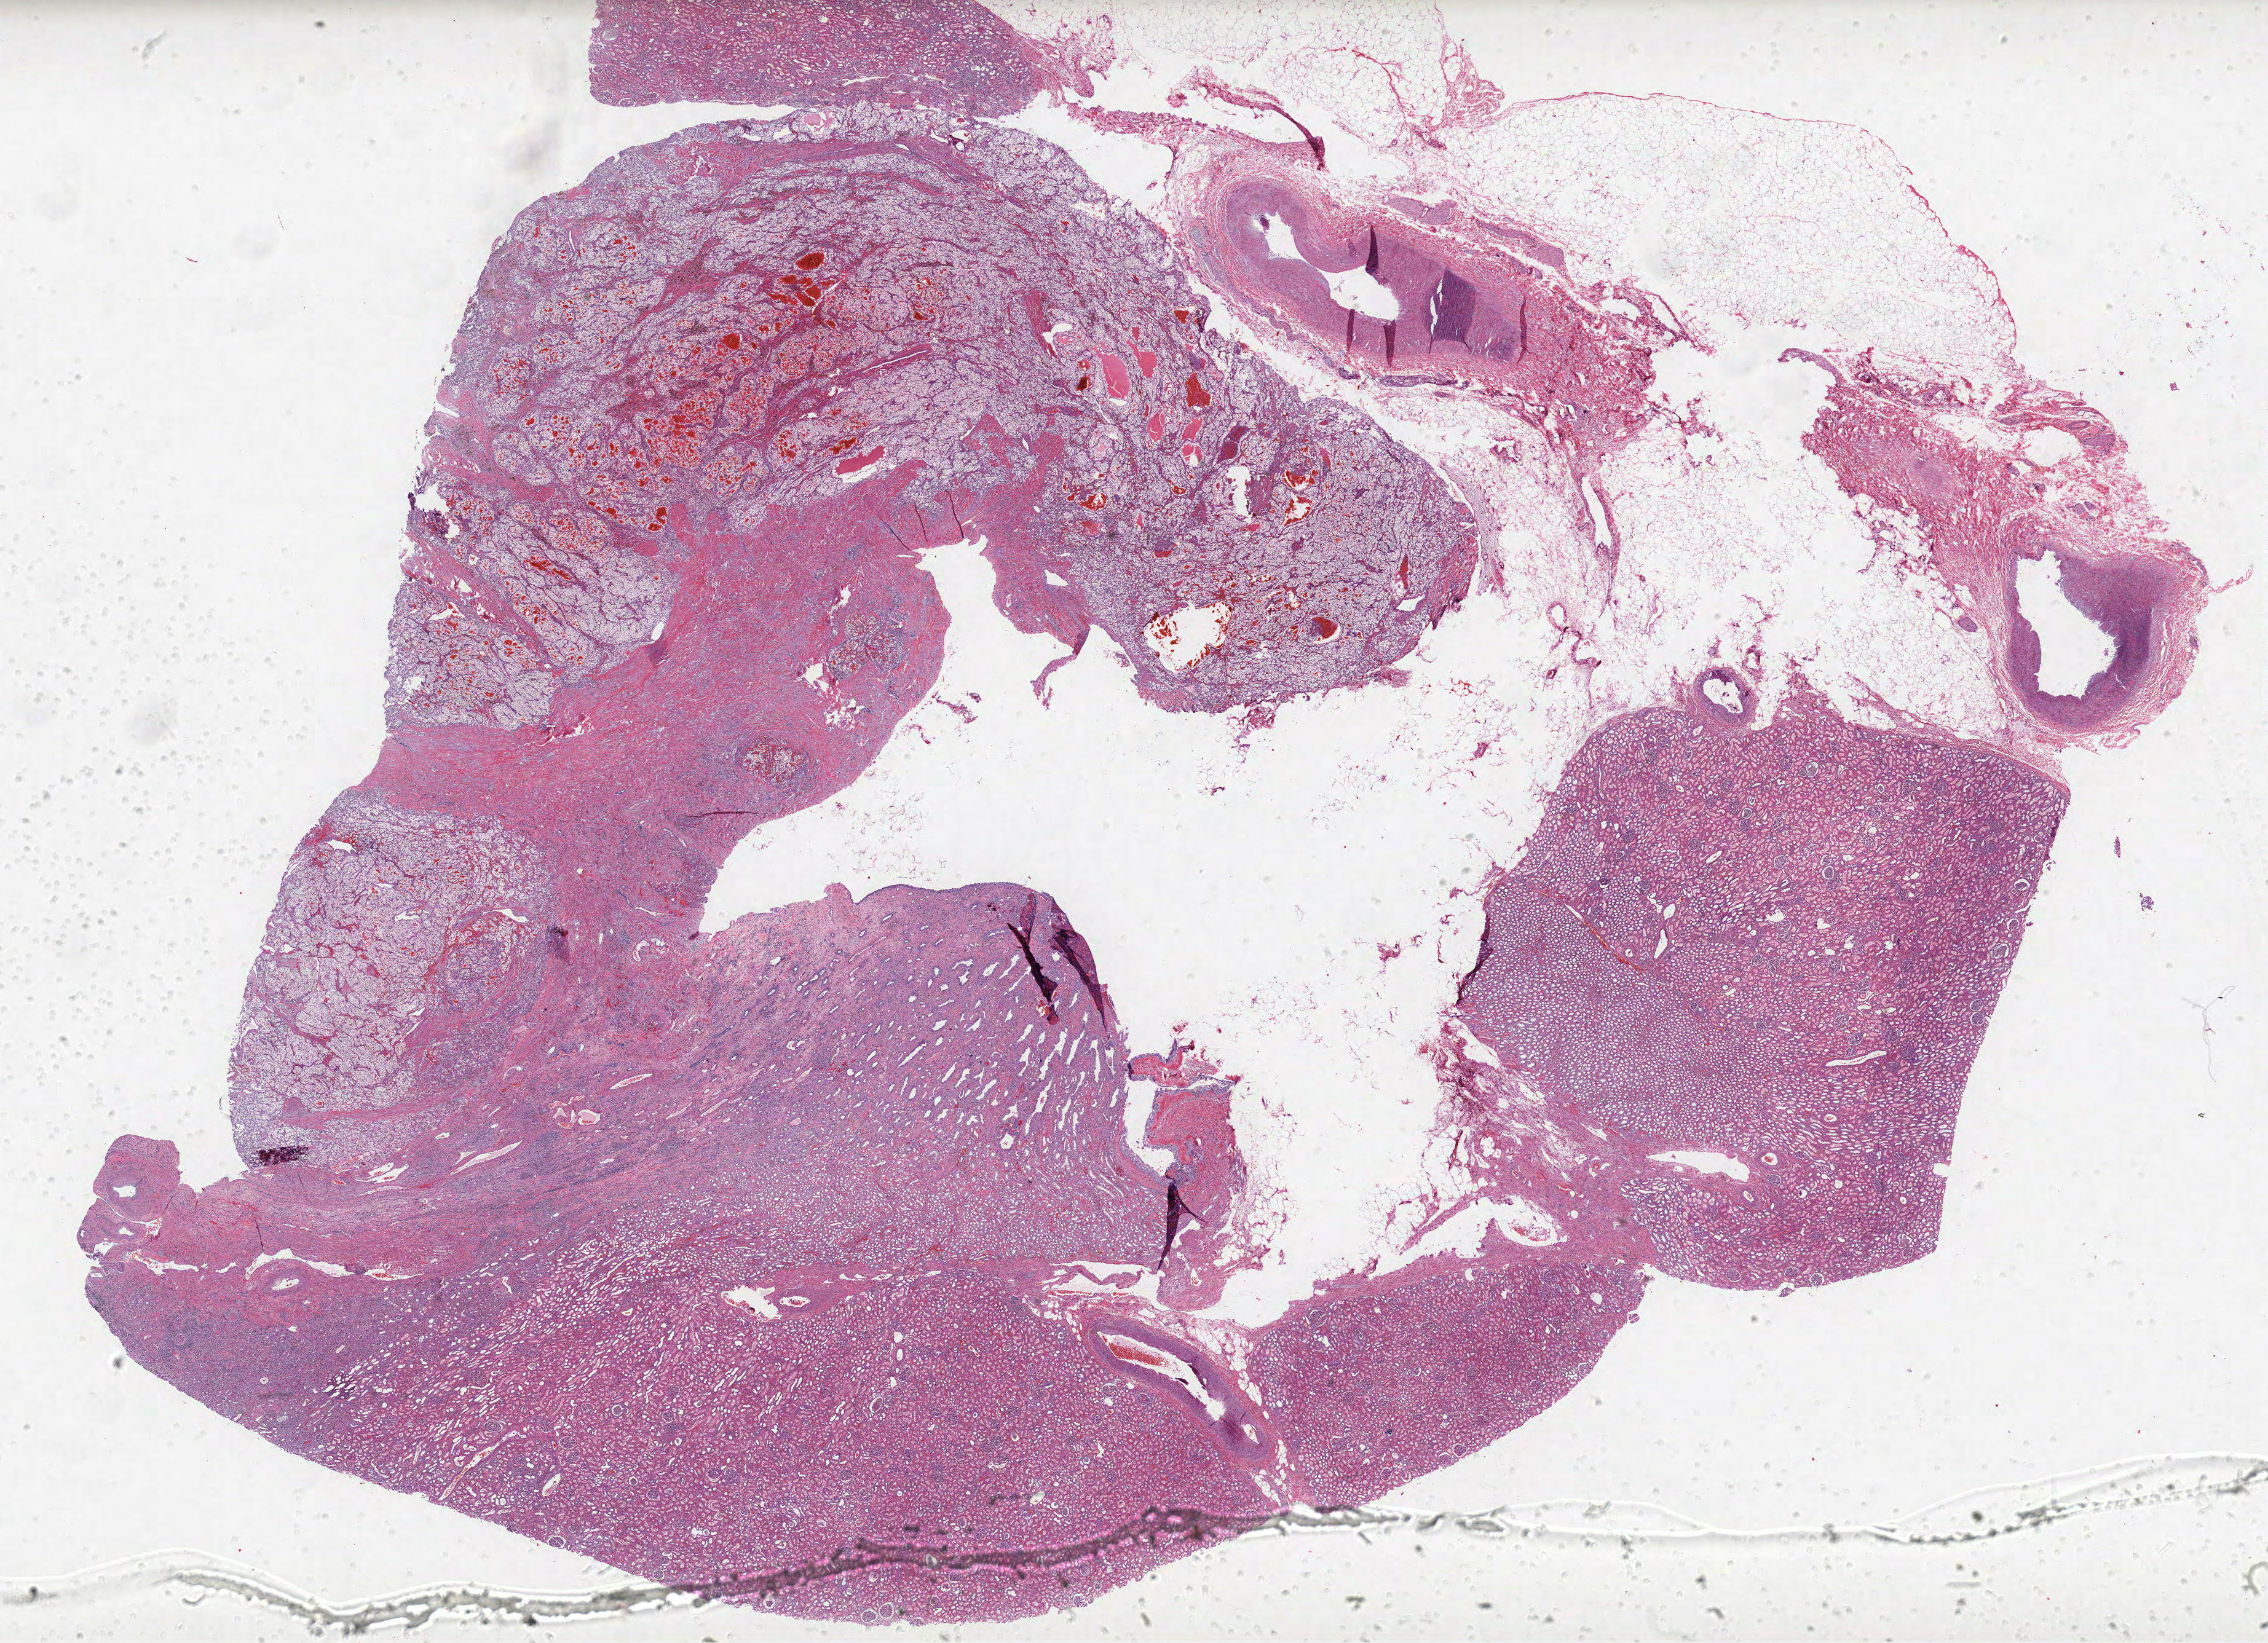
Whole-slide histology image, H&E — low-resolution overview of the scanned area, about 29.5 x 21.4 mm (slide scanned at 40x), formalin-fixed paraffin-embedded (FFPE) diagnostic section, primary tumour sample from the kidney. Male patient; age at initial diagnosis 55 years. Histologic grade: G2 (moderately differentiated).
Histologic diagnosis: Clear cell adenocarcinoma, NOS. AJCC pathologic stage: I.